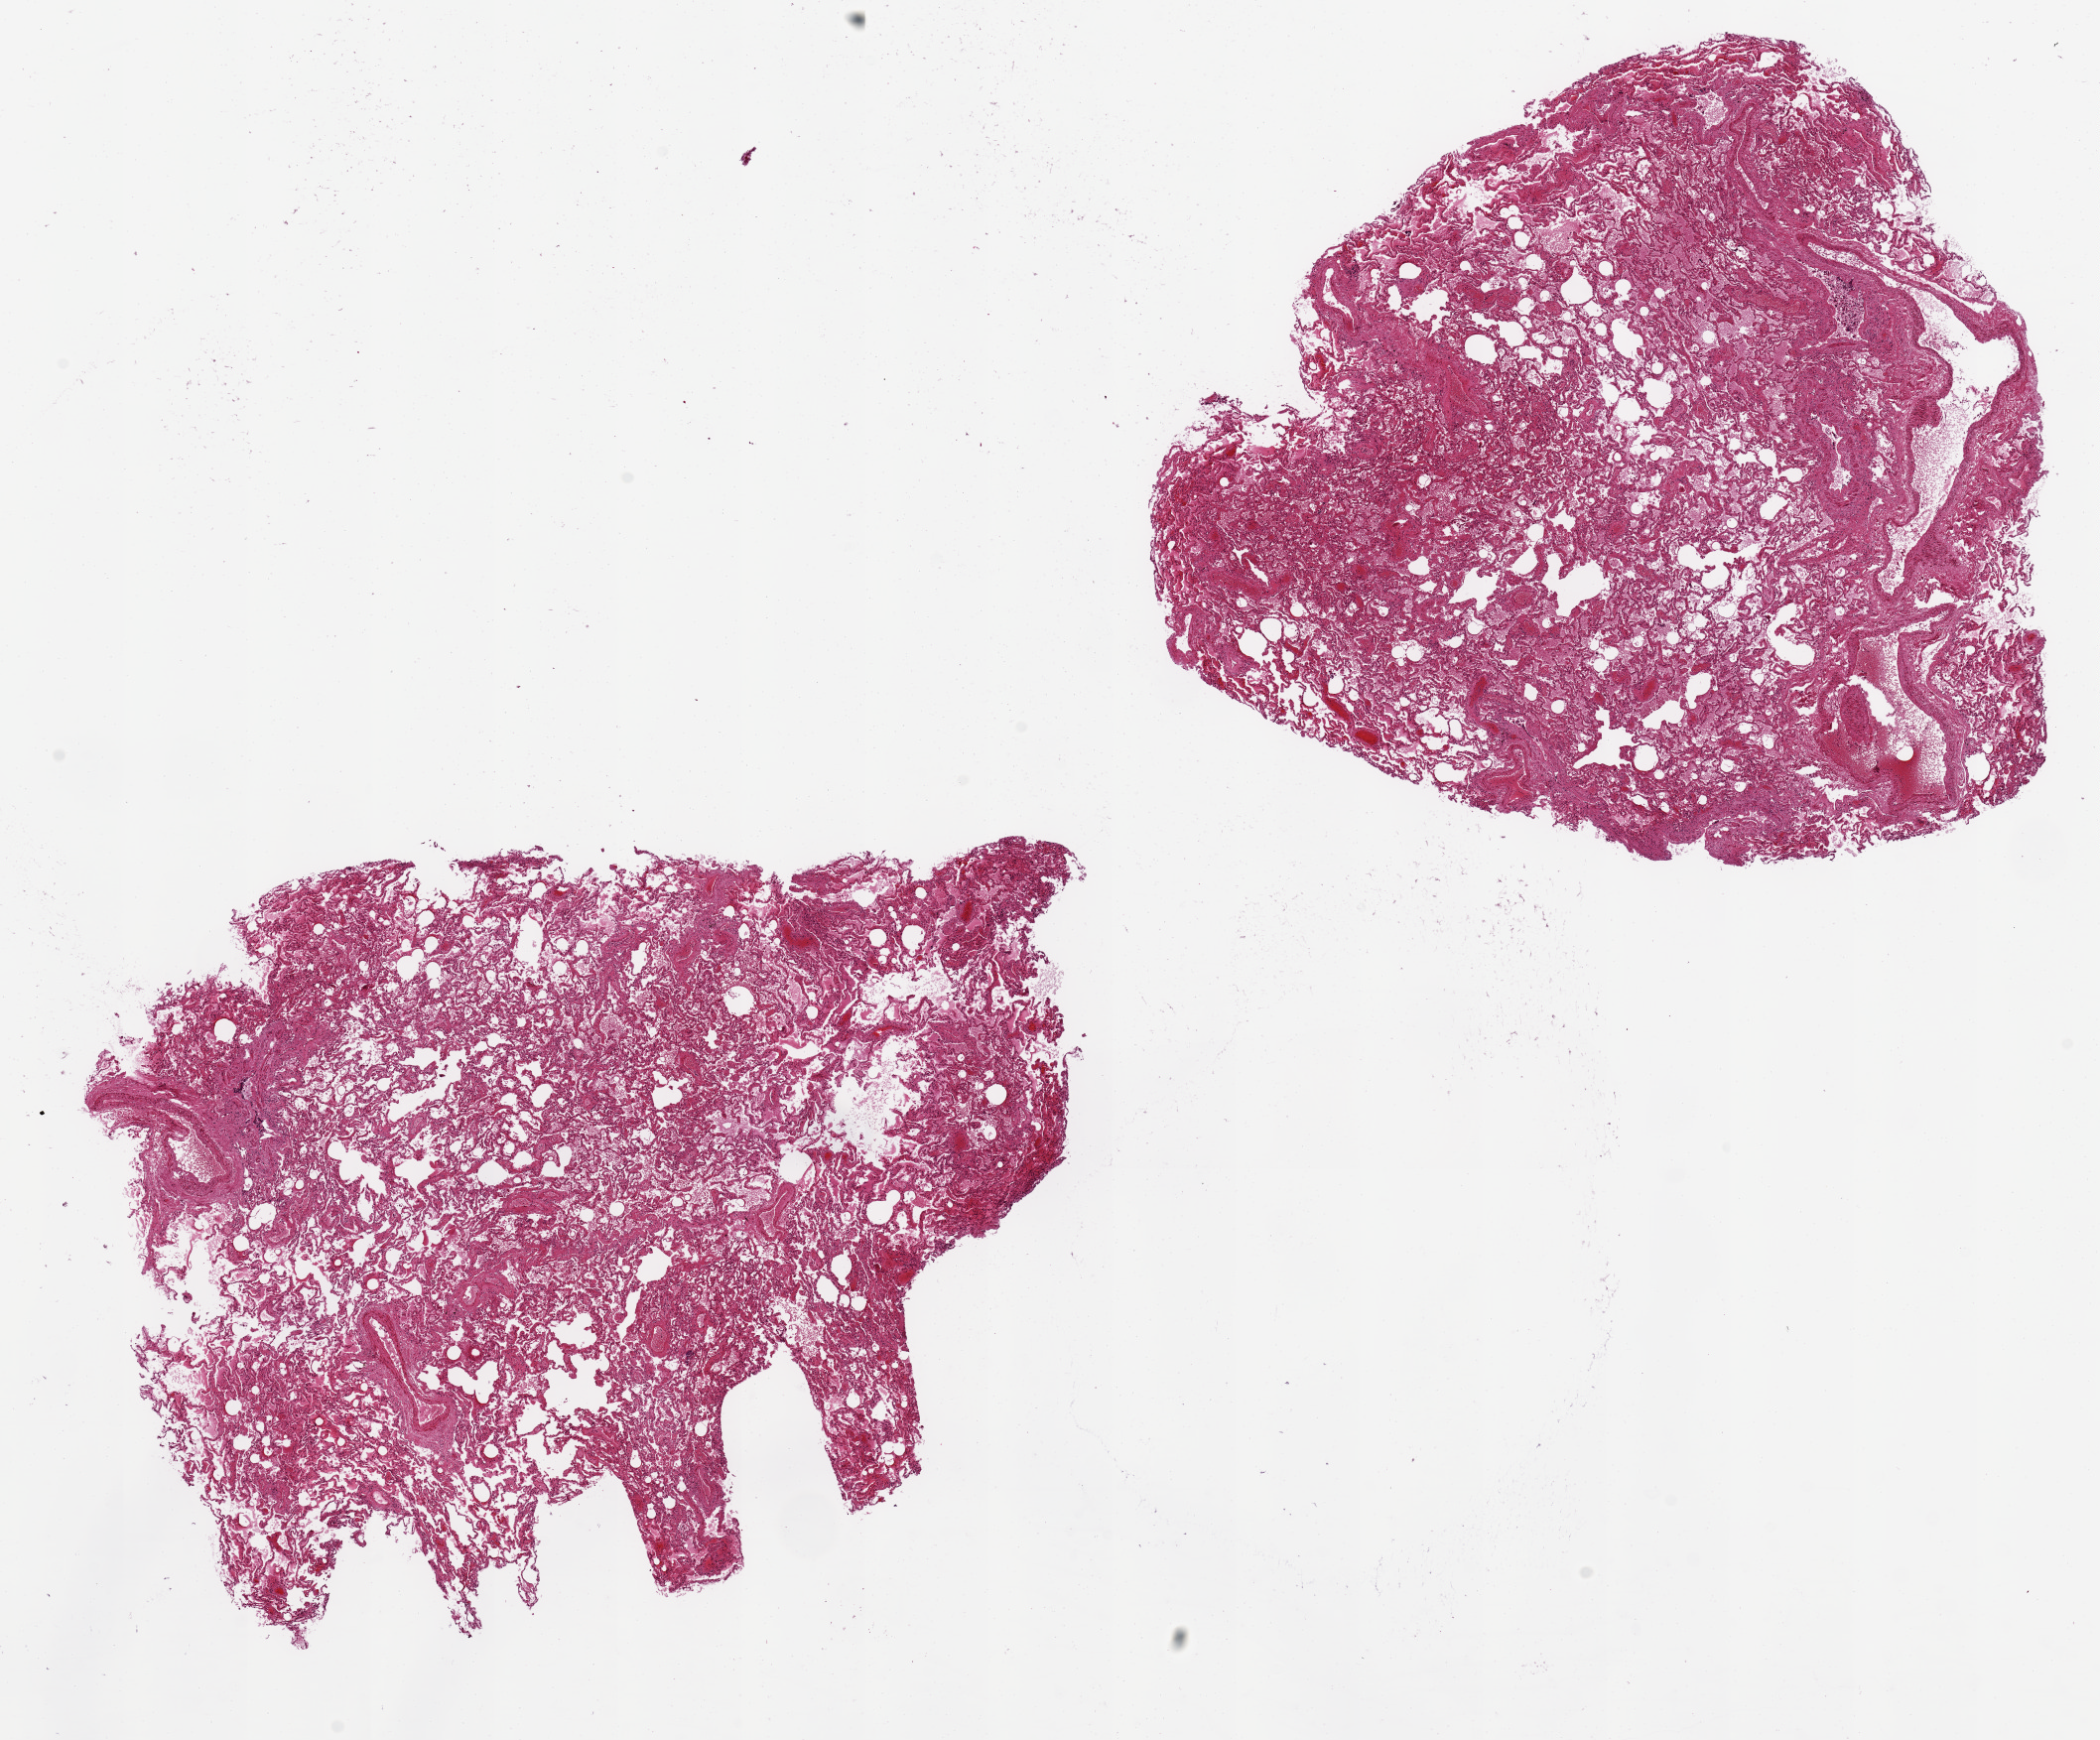
Hematoxylin and eosin (H&E) whole-slide image — shown as a low-resolution overview of the whole scanned area (about 16.7 x 13.9 mm, acquisition: 20x scan), PAXgene-fixed paraffin-embedded (PFPE) section, section of lung (target tissue), donor tissue sample. Donor sex: male.
• review note (as recorded): 2 aliquots, ~8x7mm. Diffuse patchy congestion. Moderately autolyzed